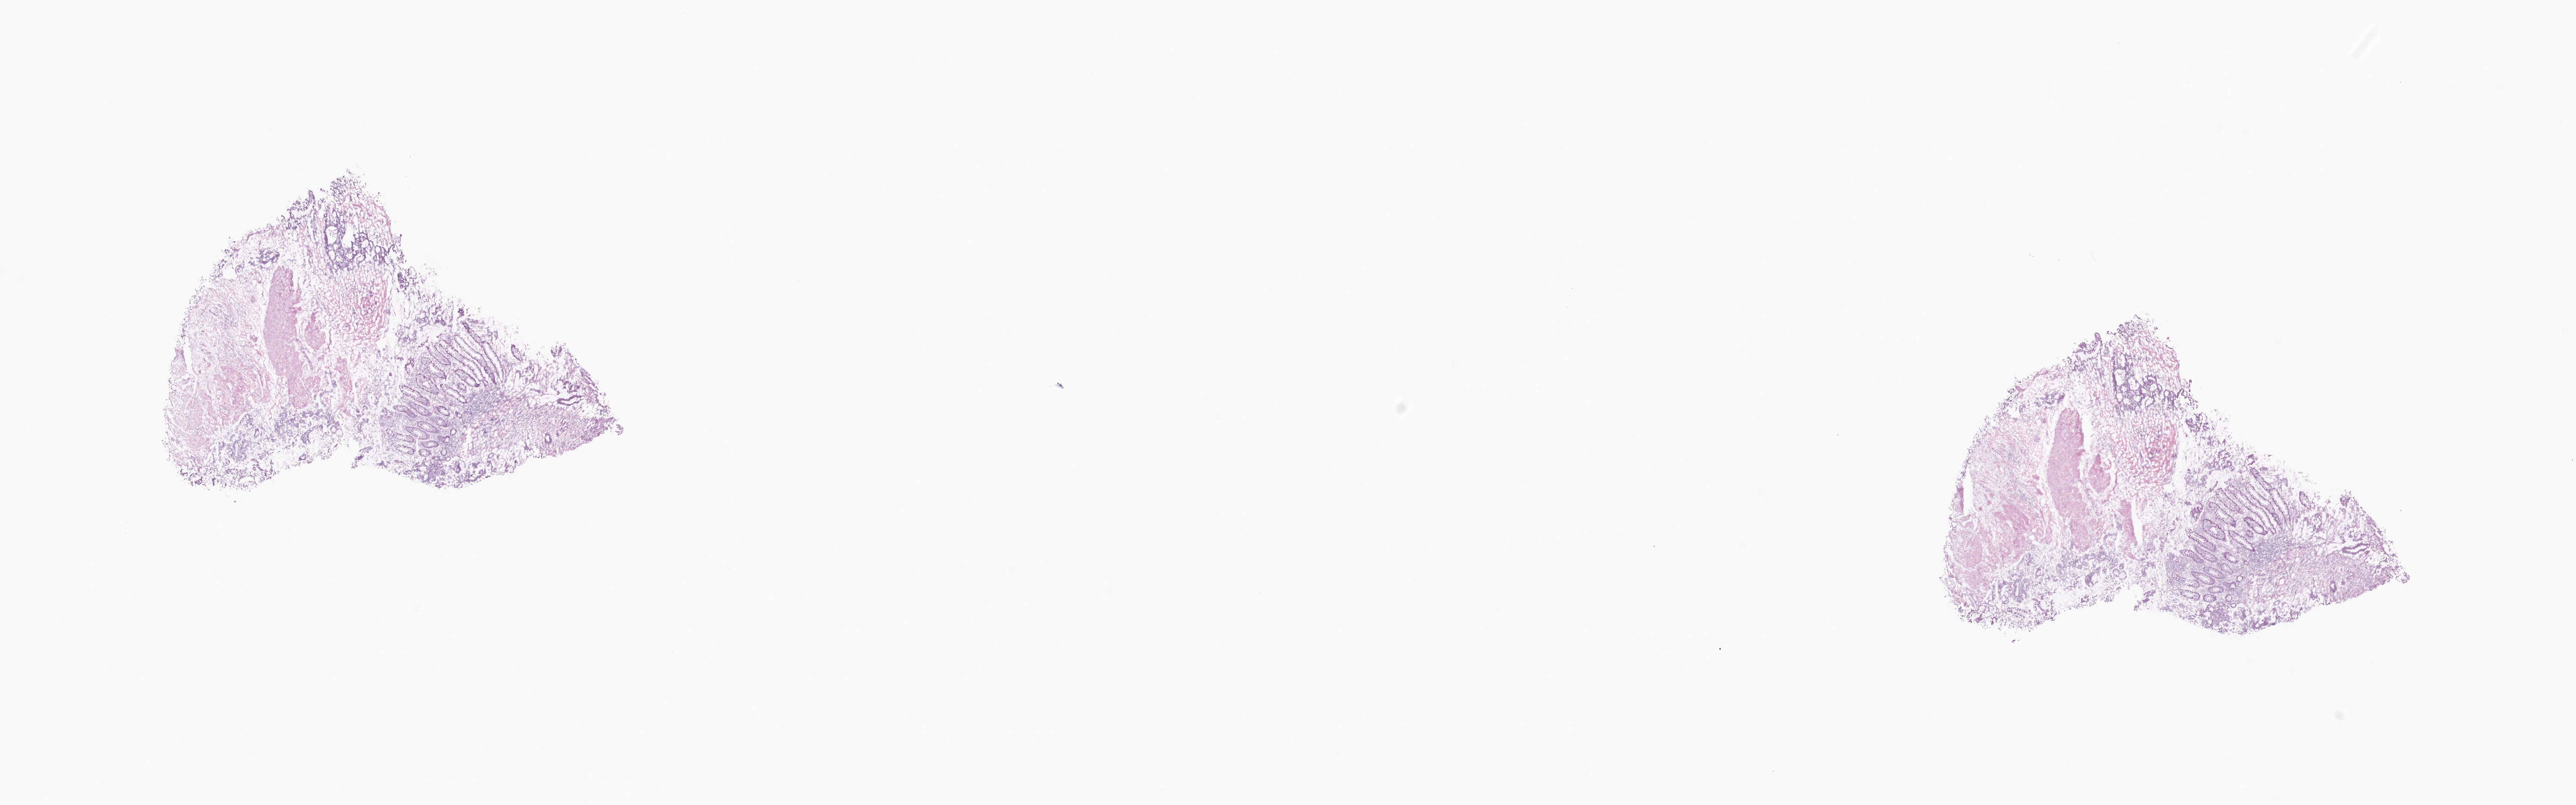
H&E whole-slide image, low-resolution overview of the scanned area, about 29.0 x 9.1 mm. Frozen section (tissue freezing medium). Primary tumor. Anatomic site: cecum. Male patient; age at initial diagnosis 72 years. Pathologist review of this section (percent, as recorded): tumor cells 19%, tumor nuclei 25%, stromal cells 23%, necrosis 1%, normal cells 57%. Infiltration values recorded for this section: lymphocyte infiltration 18%, monocyte infiltration 7%, neutrophil infiltration 0%.
• section: bottom of the tissue portion
• histologic diagnosis: Adenocarcinoma, NOS